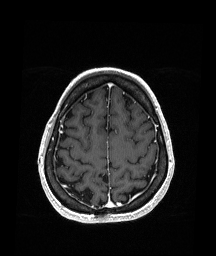
Brain MRI from a brain-tumour surgery series, one axial slice. Position 54 of 151 along the scan axis. T1-weighted post-contrast. 1.05 mm slice thickness. 216 × 256 image matrix, field of view 211 × 250 mm. From the clinical record (not read from this slice): histopathology: Oligodendroglioma; WHO grade: 2; IDH mutation: yes; tumour location: Right Parietal.
Structures marked on this image (outlined manually by an expert reader):
- previous resection cavity: bounding box [x1, y1, x2, y2] px = [99, 172, 109, 181]